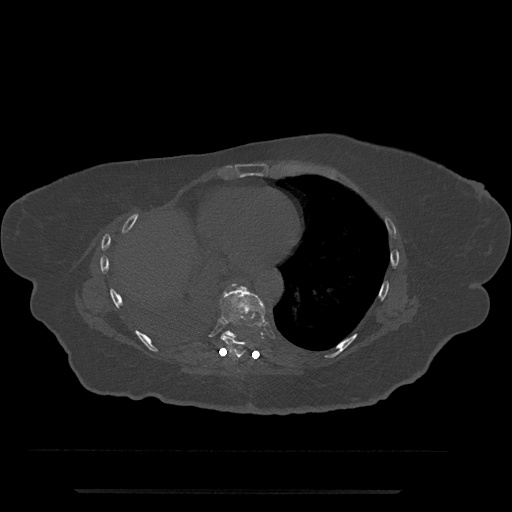
CT including the spine, one axial slice; position 378 of 797 along the scan axis; bone window (W 1800 / L 400 HU); 0.5 mm slice thickness; 512 × 512 image matrix, field of view 440 × 440 mm. Patient: female, 51 years. Case-level facts recorded for this patient, not image findings: primary cancer: neuro; vertebrae with lytic lesions (as recorded): T8.
Structures marked on this image (semi-automatically segmented with operator editing):
- T7 vertebra: box from (x=238, y=370) to (x=240, y=372) px
- T8 vertebra: (x=219, y=283)–(x=265, y=359)
- T9 vertebra: (x=218, y=286)–(x=265, y=340)